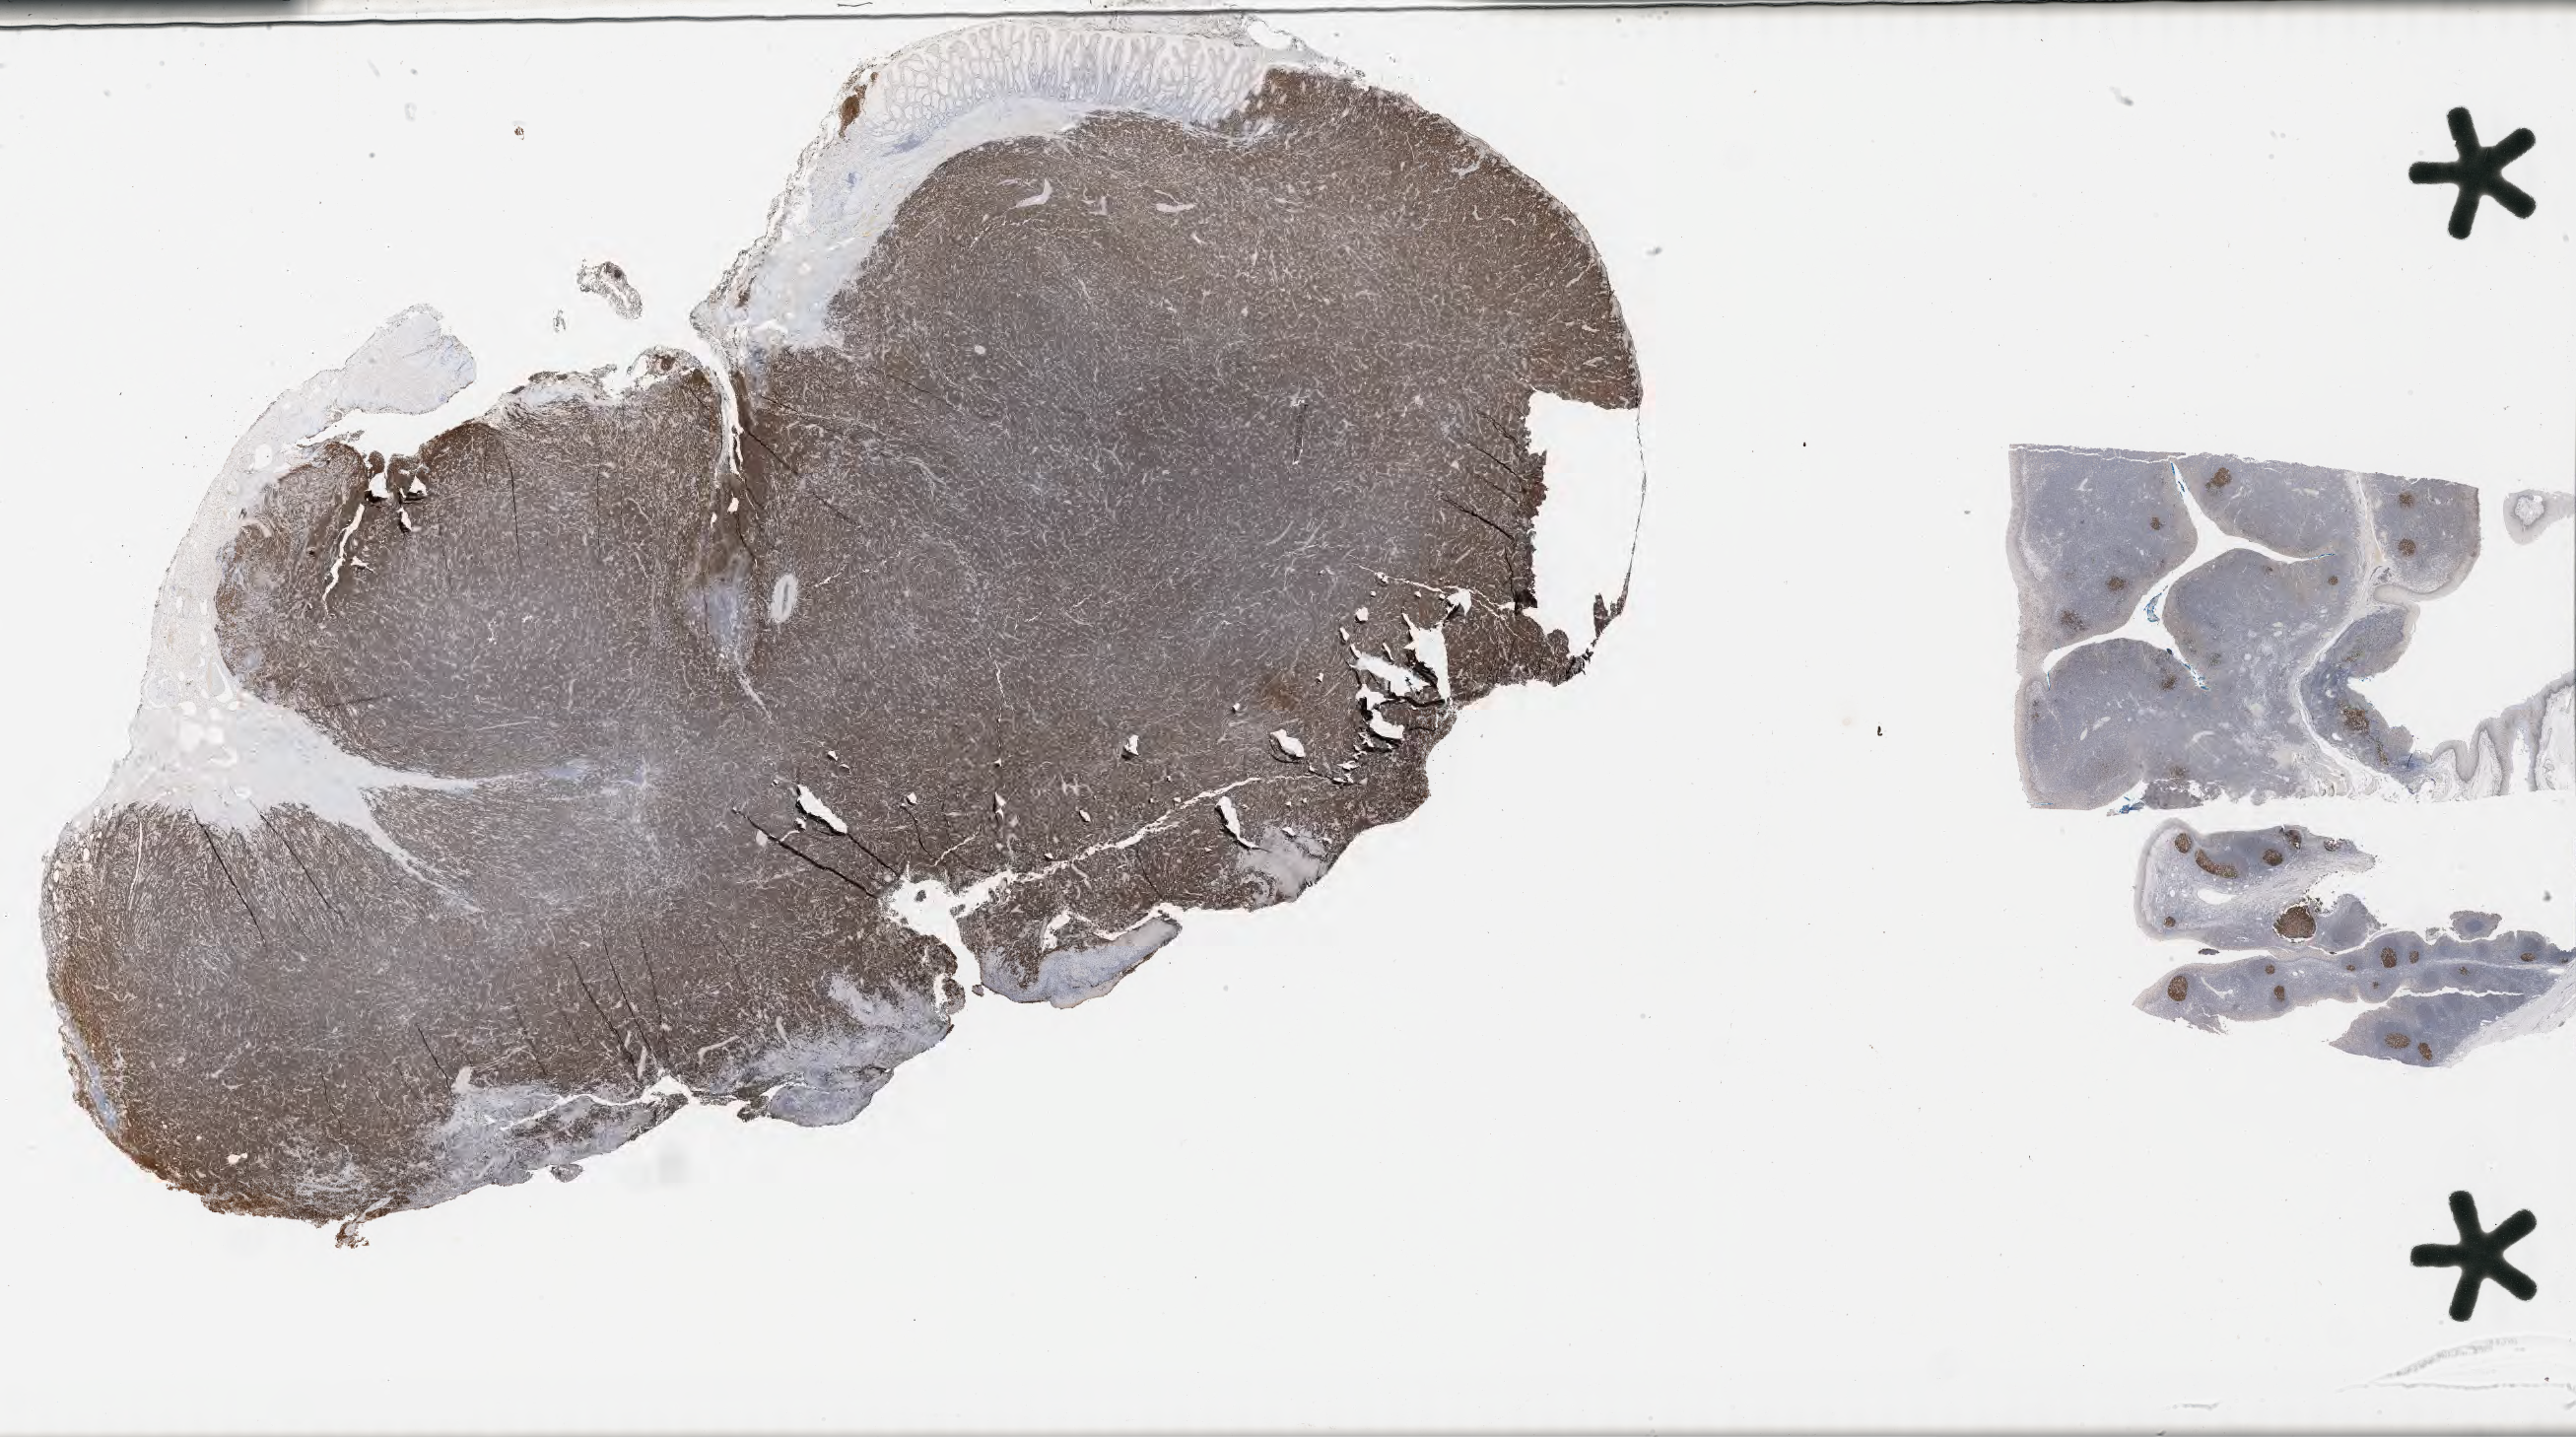
Immunohistochemistry (IHC) whole-slide image stained for BCL6, a low-resolution overview of the entire scanned area, about 42.3 x 23.6 mm. Tumor tissue. Patient female; aged 29.
Diagnosis: Burkitt lymphoma, NOS.